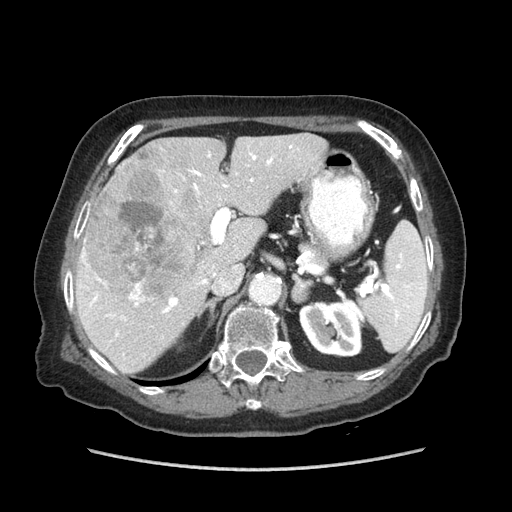
Contrast-enhanced abdominal CT (liver protocol), one axial slice. Slice 48 of 89 in the series (ordered by position). Soft-tissue window (W 400 / L 40 HU). 512 × 512 image matrix, field of view 360 × 360 mm. From the clinical record (not read from this slice): diagnosis: hepatocellular carcinoma (patient treated with transarterial chemoembolisation; whether this scan precedes or follows treatment is not stated here); TNM stage (as recorded): Stage-IIIA; Child-Pugh class: A; tumour differentiation: well differentiated; tumour size: 11 cm.
Annotated regions visible in this slice (semi-automatically segmented with operator editing):
- liver parenchyma outside the tumour (the mass and vessels are separate outlines, so this box may not span the whole liver): bounding box <76,134,326,374> (left, top, right, bottom; pixels)
- mass: <84,160,205,297>
- liver vessels: <79,146,292,337>